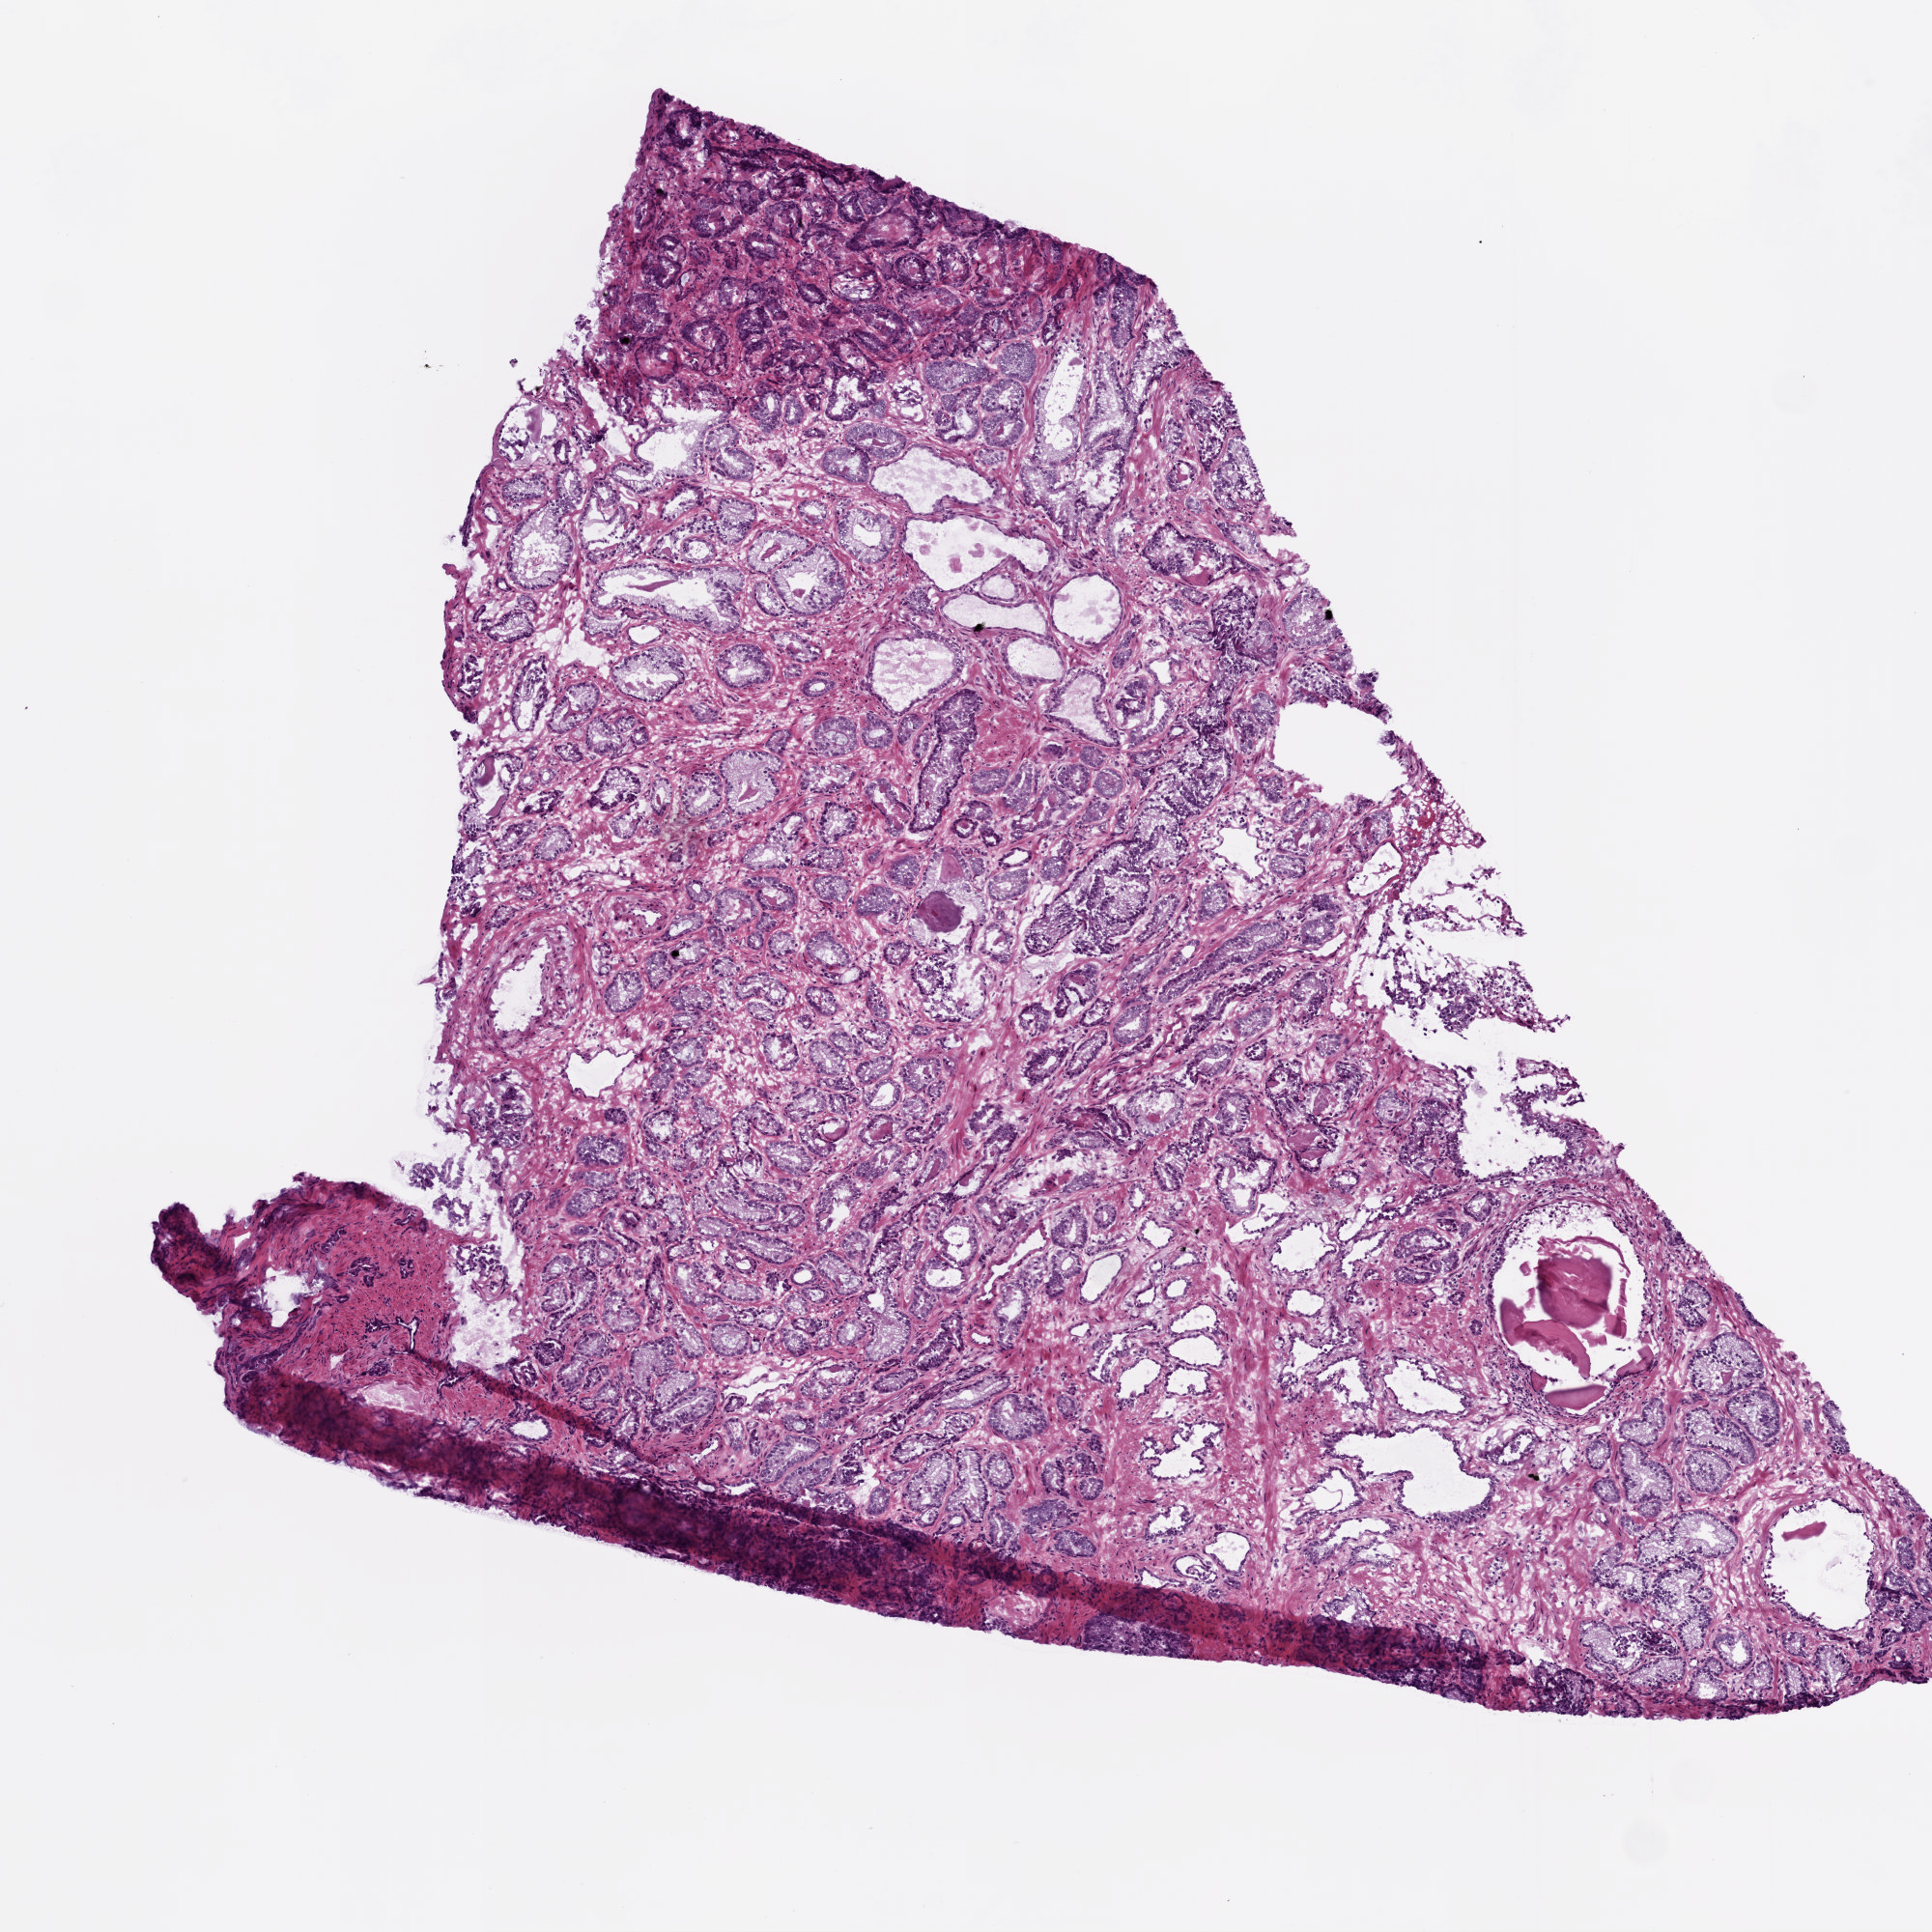
H&E-stained whole-slide image, shown as a low-resolution overview of the whole scanned area (about 4.0 x 4.0 mm, slide scanned at 20x). Frozen section. Prostate, primary tumour sample. Male patient; age at initial diagnosis 64 years. Gleason score: 7 (3+4). Slide review estimates, as recorded: tumour cells 65%, tumour nuclei 75%, normal cells 20%, stromal cells 15%, necrosis 0%. Inflammatory infiltration, as recorded: lymphocyte infiltration 0%, monocyte infiltration 0%, neutrophil infiltration 0%.
- pathologic diagnosis: Acinar cell carcinoma (prostate gland)